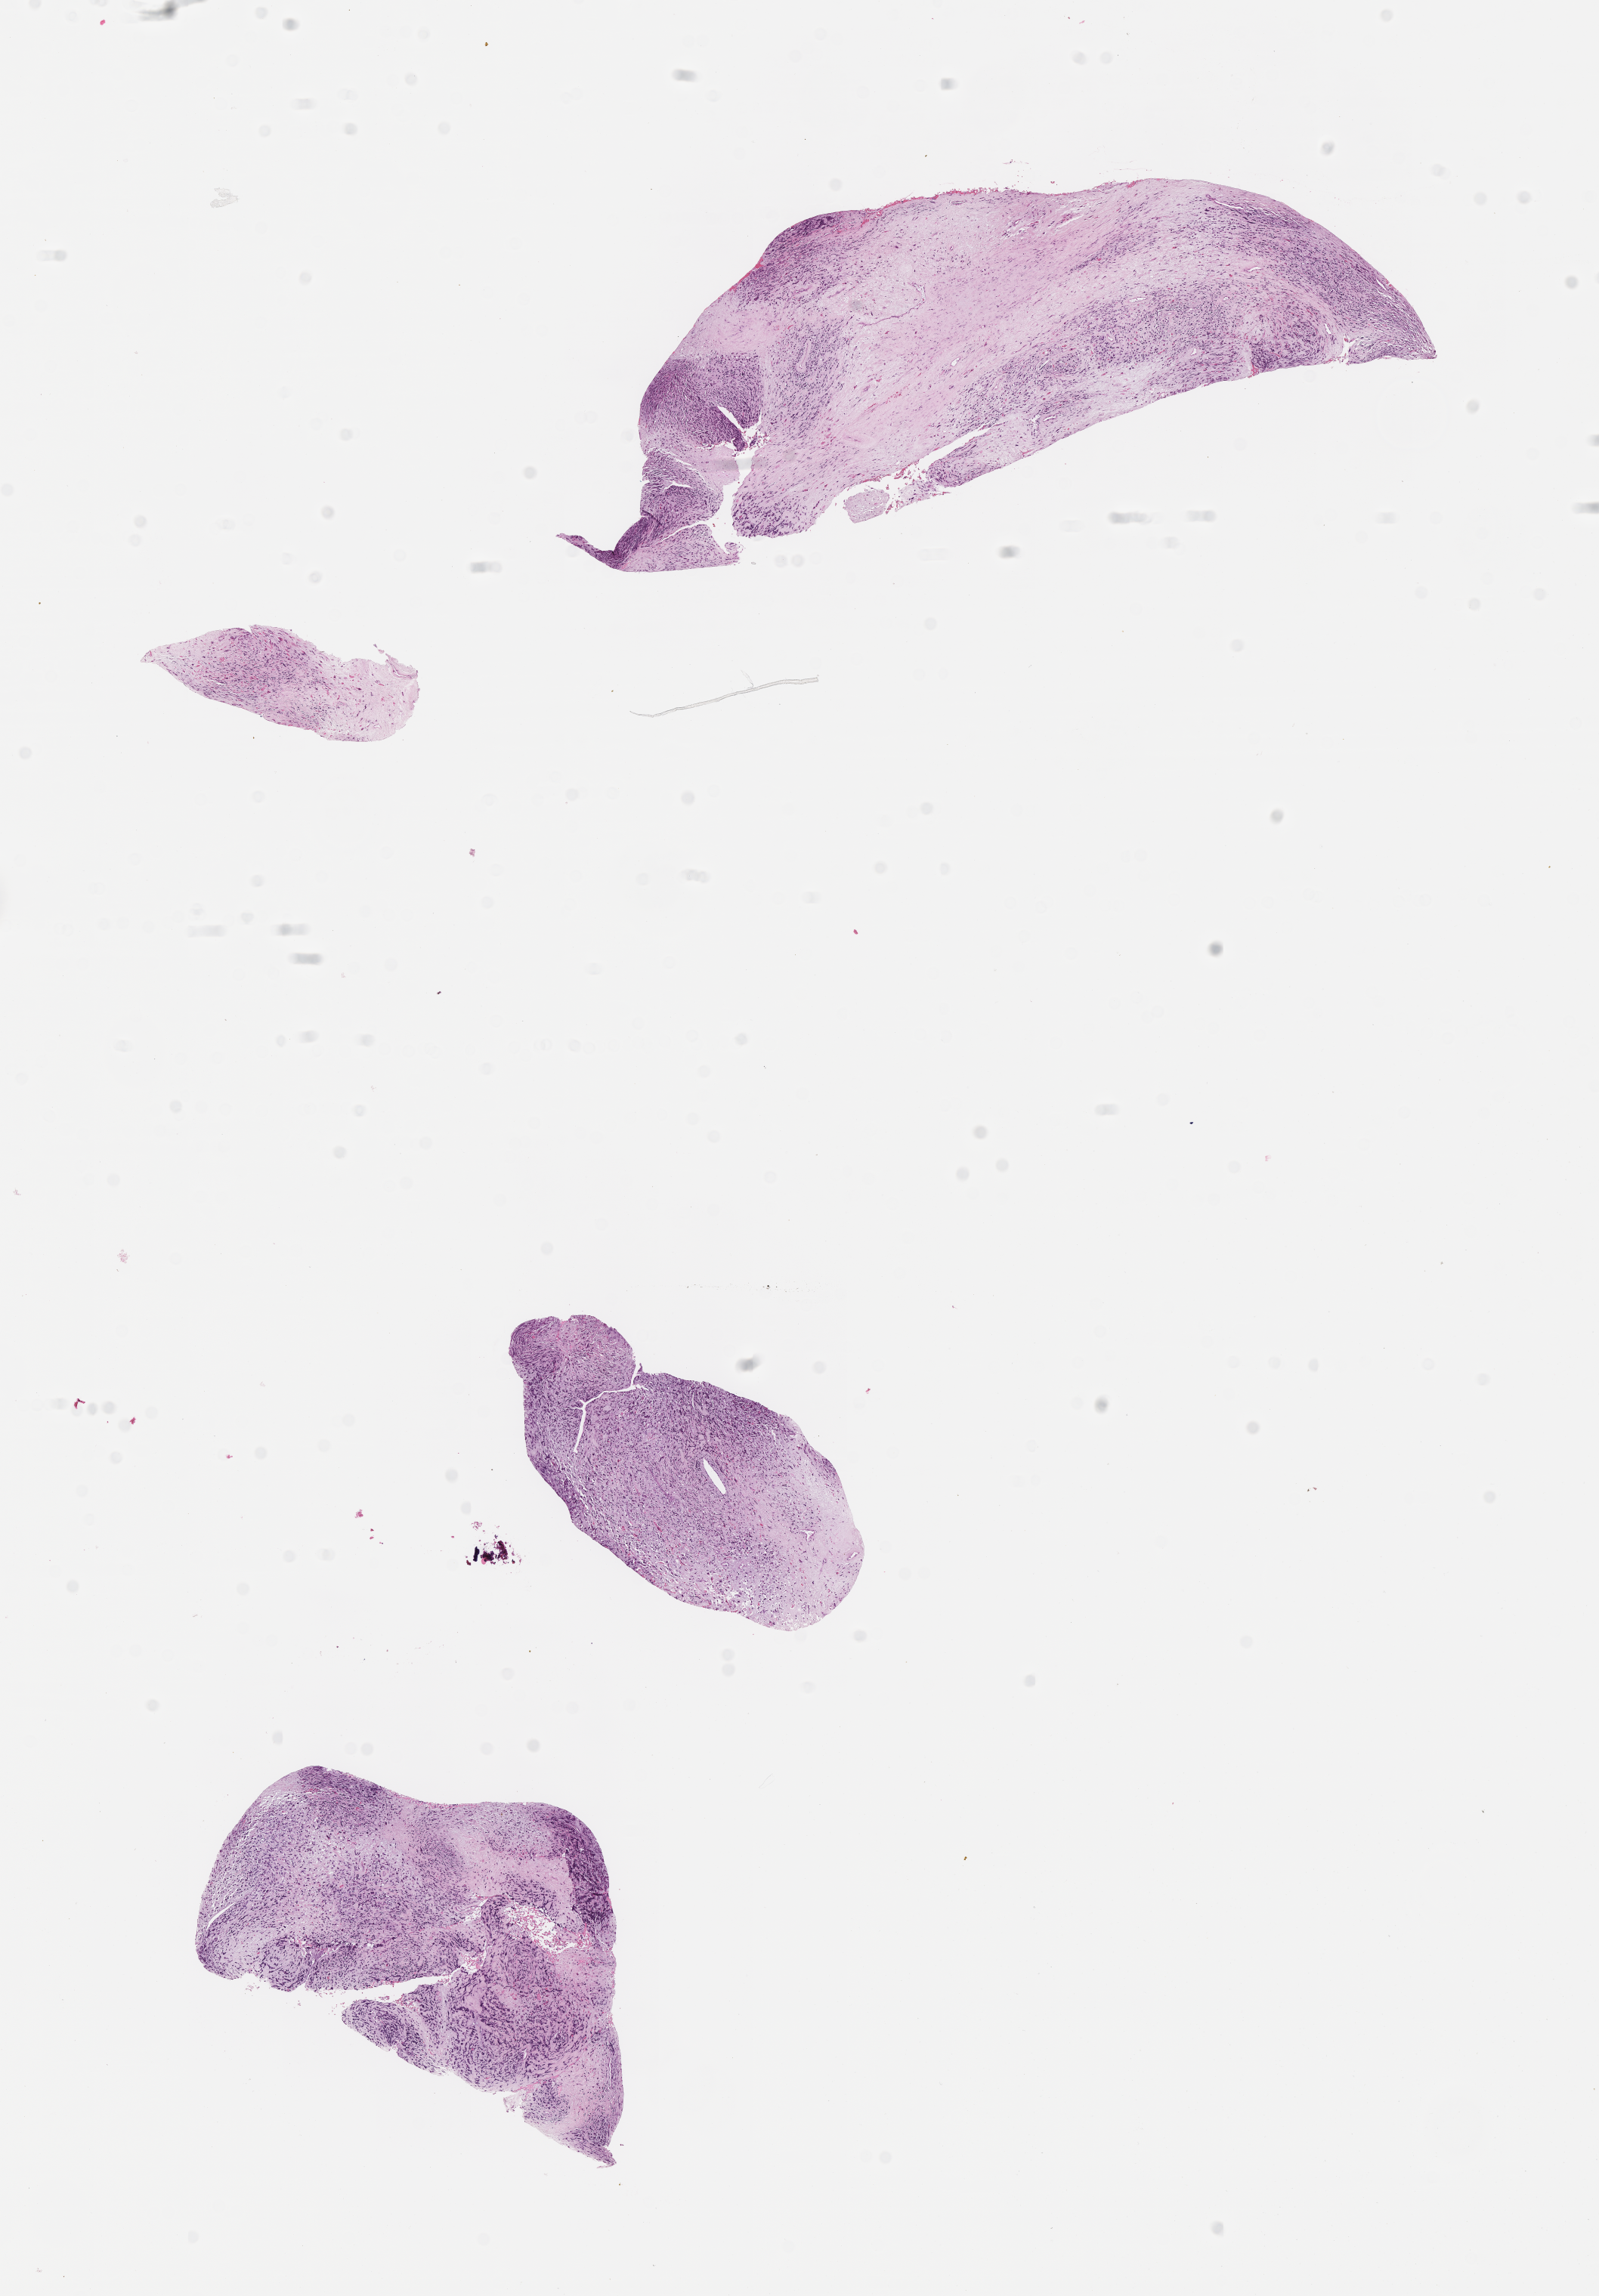
Haematoxylin and eosin whole-slide image of tumor tissue, whole scanned area (about 8.6 x 12.3 mm) shown as a low-resolution overview; formalin-fixed paraffin-embedded section; sample anatomic site: soft tissue, shoulder-left. Male patient, age at diagnosis 2.3 years.
Diagnosis: rhabdomyosarcoma; histological classification: embryonal rhabdomyosarcoma.